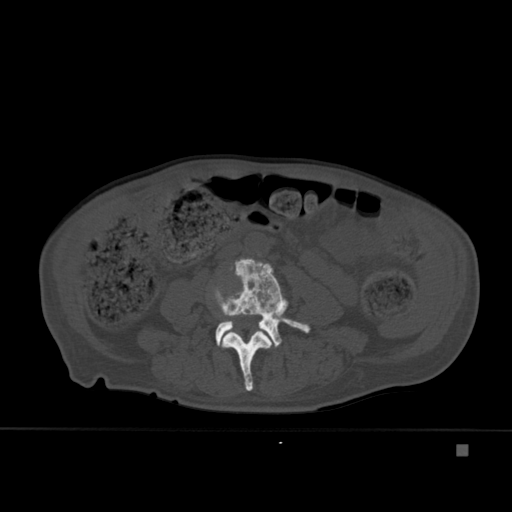
CT including the spine, one axial slice. Slice 133 of 451 in the series (ordered by position). Bone window (W 1800 / L 400 HU). 512 × 512 image matrix, field of view 378 × 378 mm. Male patient, age 75 years. From the clinical record (not read from this slice): primary cancer: prostate.
Structures marked on this image (semi-automatically segmented with operator editing):
- L3 vertebra: bounding box <221,331,272,391> (left, top, right, bottom; pixels)
- L4 vertebra: <215,258,310,348>